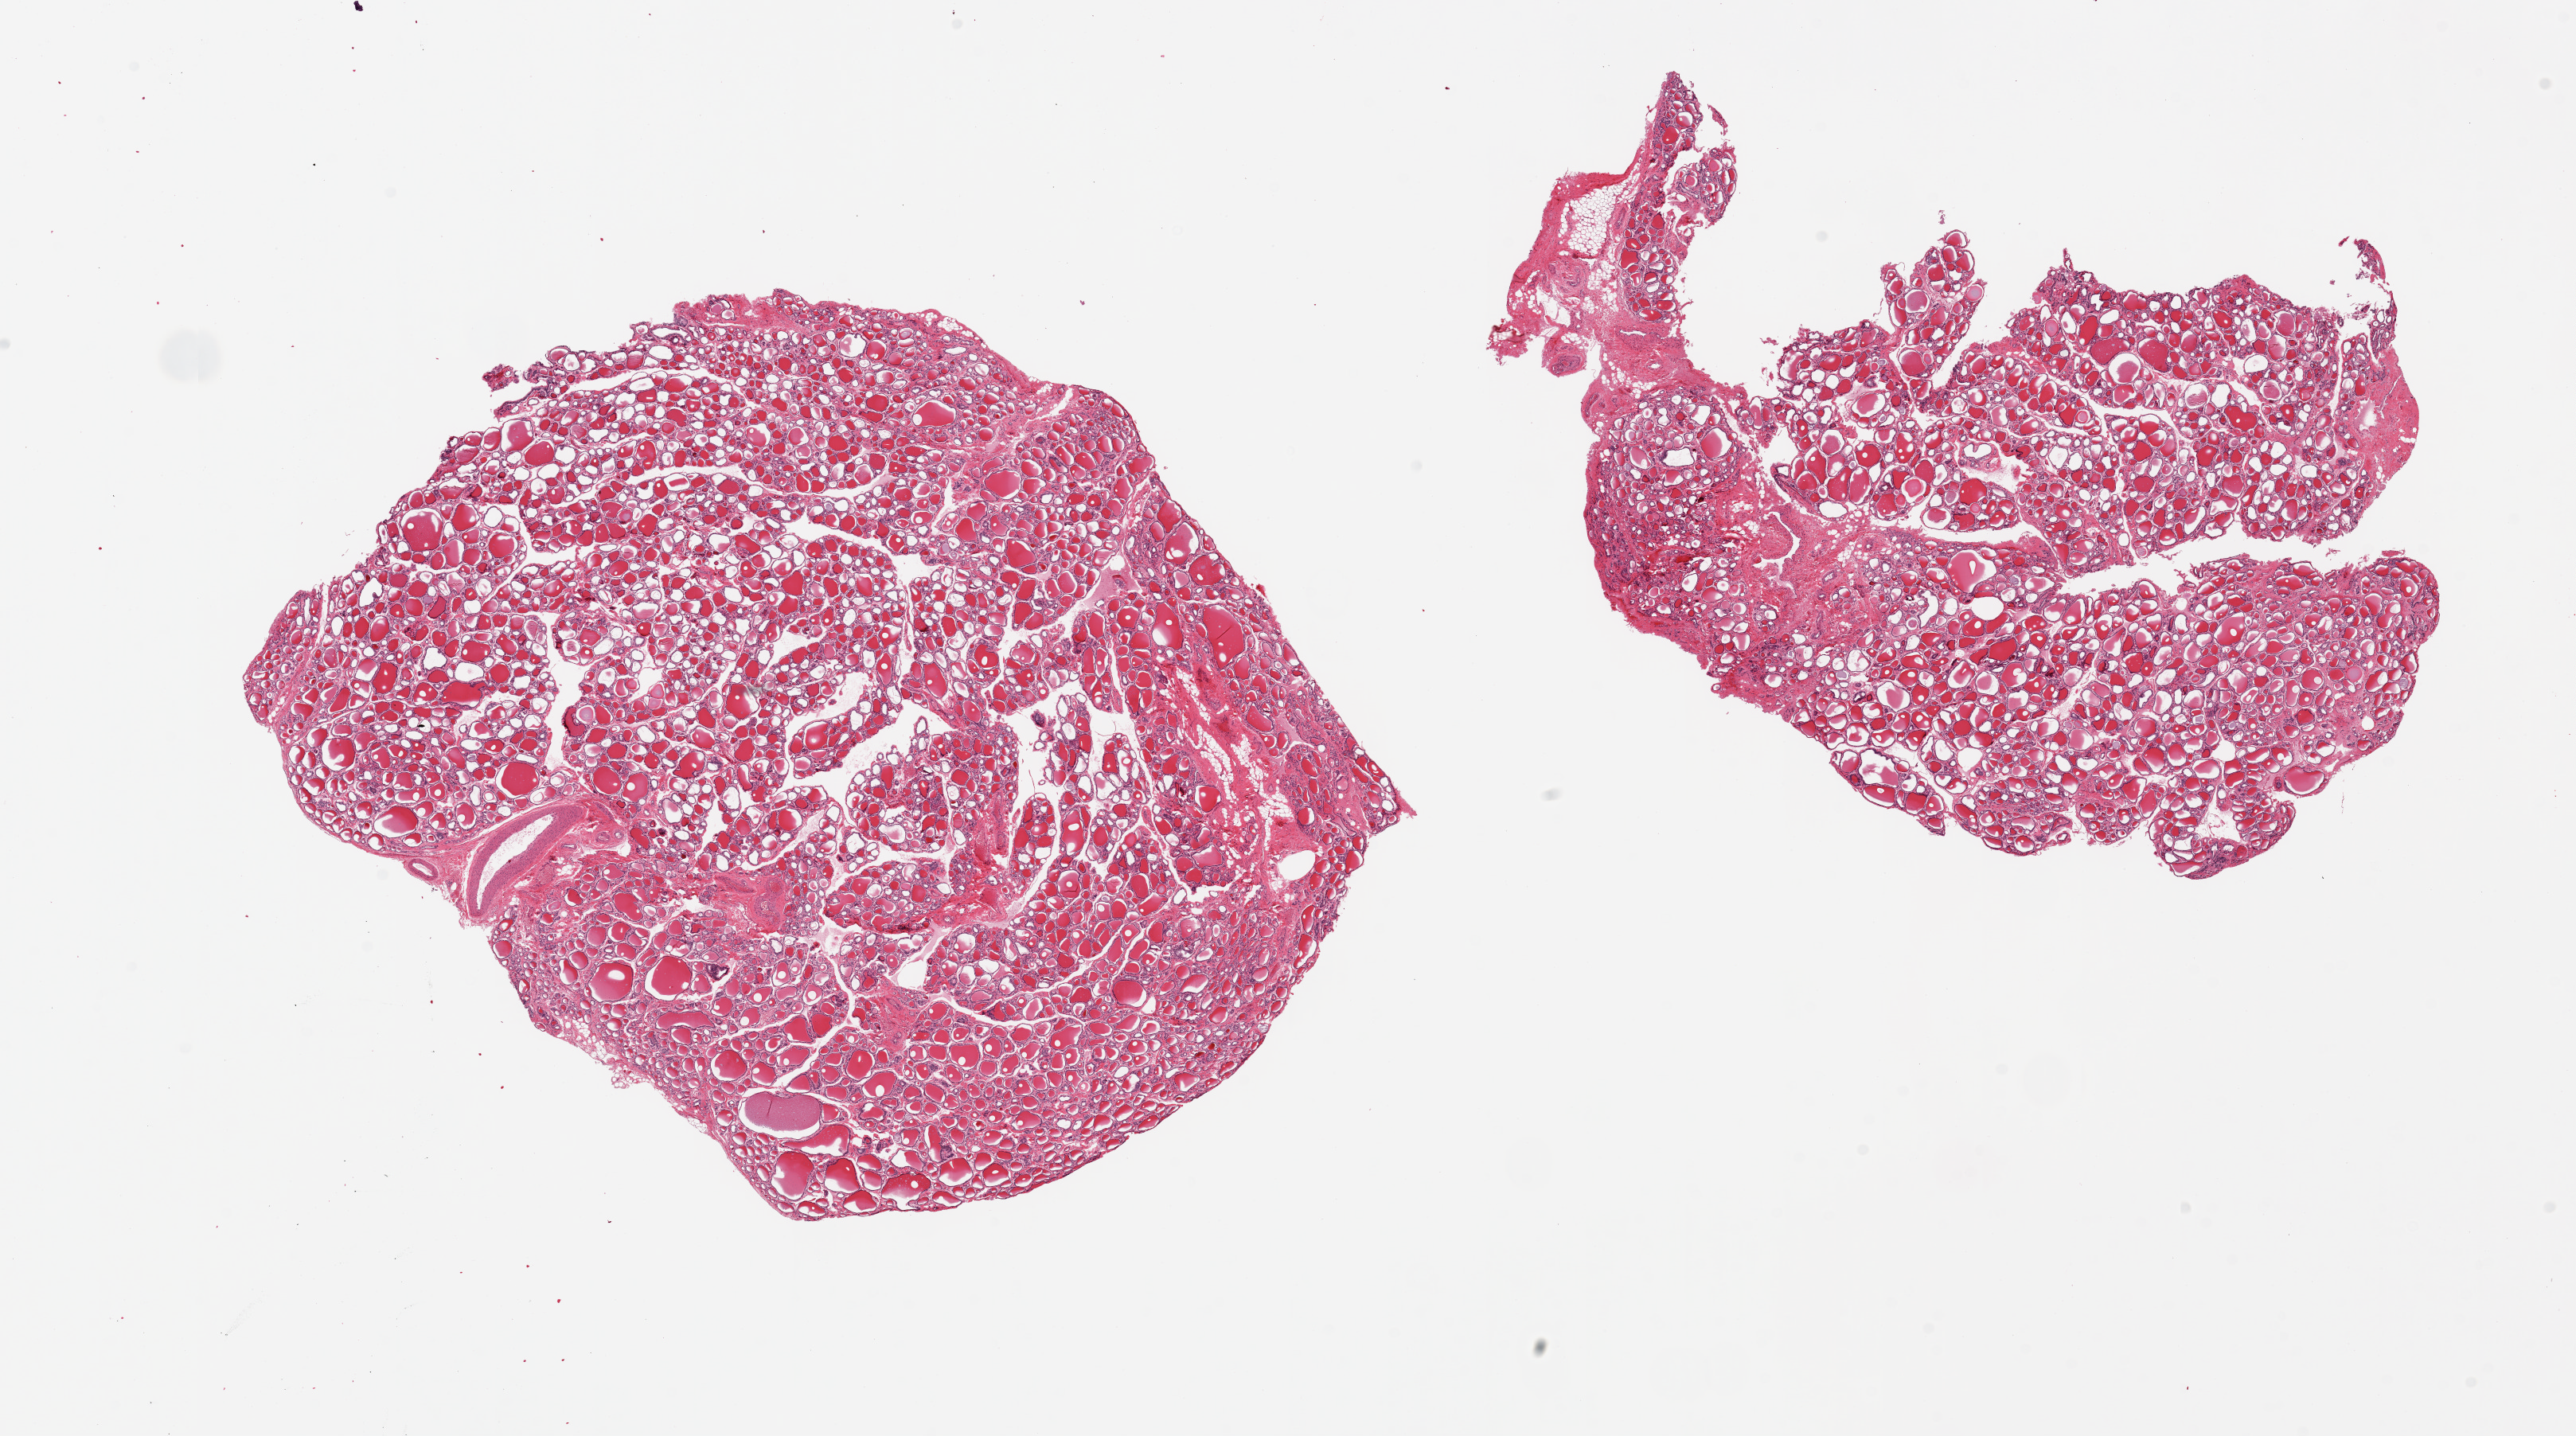
Whole-slide image, haematoxylin and eosin stain, a low-resolution overview of the entire scanned area, about 25.6 x 14.3 mm (slide scanned at 20x); PAXgene-fixed, paraffin-embedded tissue; target tissue: thyroid; tissue donor sample.
Reviewer comment on this tissue sample: 2 pieces, one piece has small attachment of adipose and fibrovascular tissue, focal adipose metaplasia of stroma.